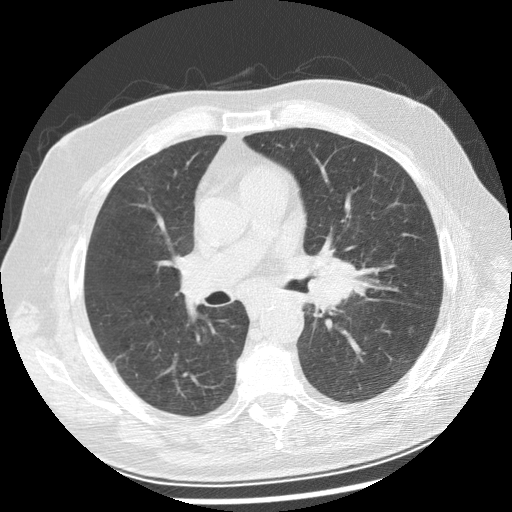
Low-dose screening chest CT, one axial slice. Slice 142 of 250 in the series (ordered by position). Lung window (W 1500 / L -600 HU). 2.5 mm slice thickness. 512 × 512 image matrix, field of view 360 × 360 mm.
Outlined on this slice (expert manual segmentation):
- lesion 1 (tumor, left main bronchus): bounding box [x1, y1, x2, y2] px = [309, 256, 366, 313]